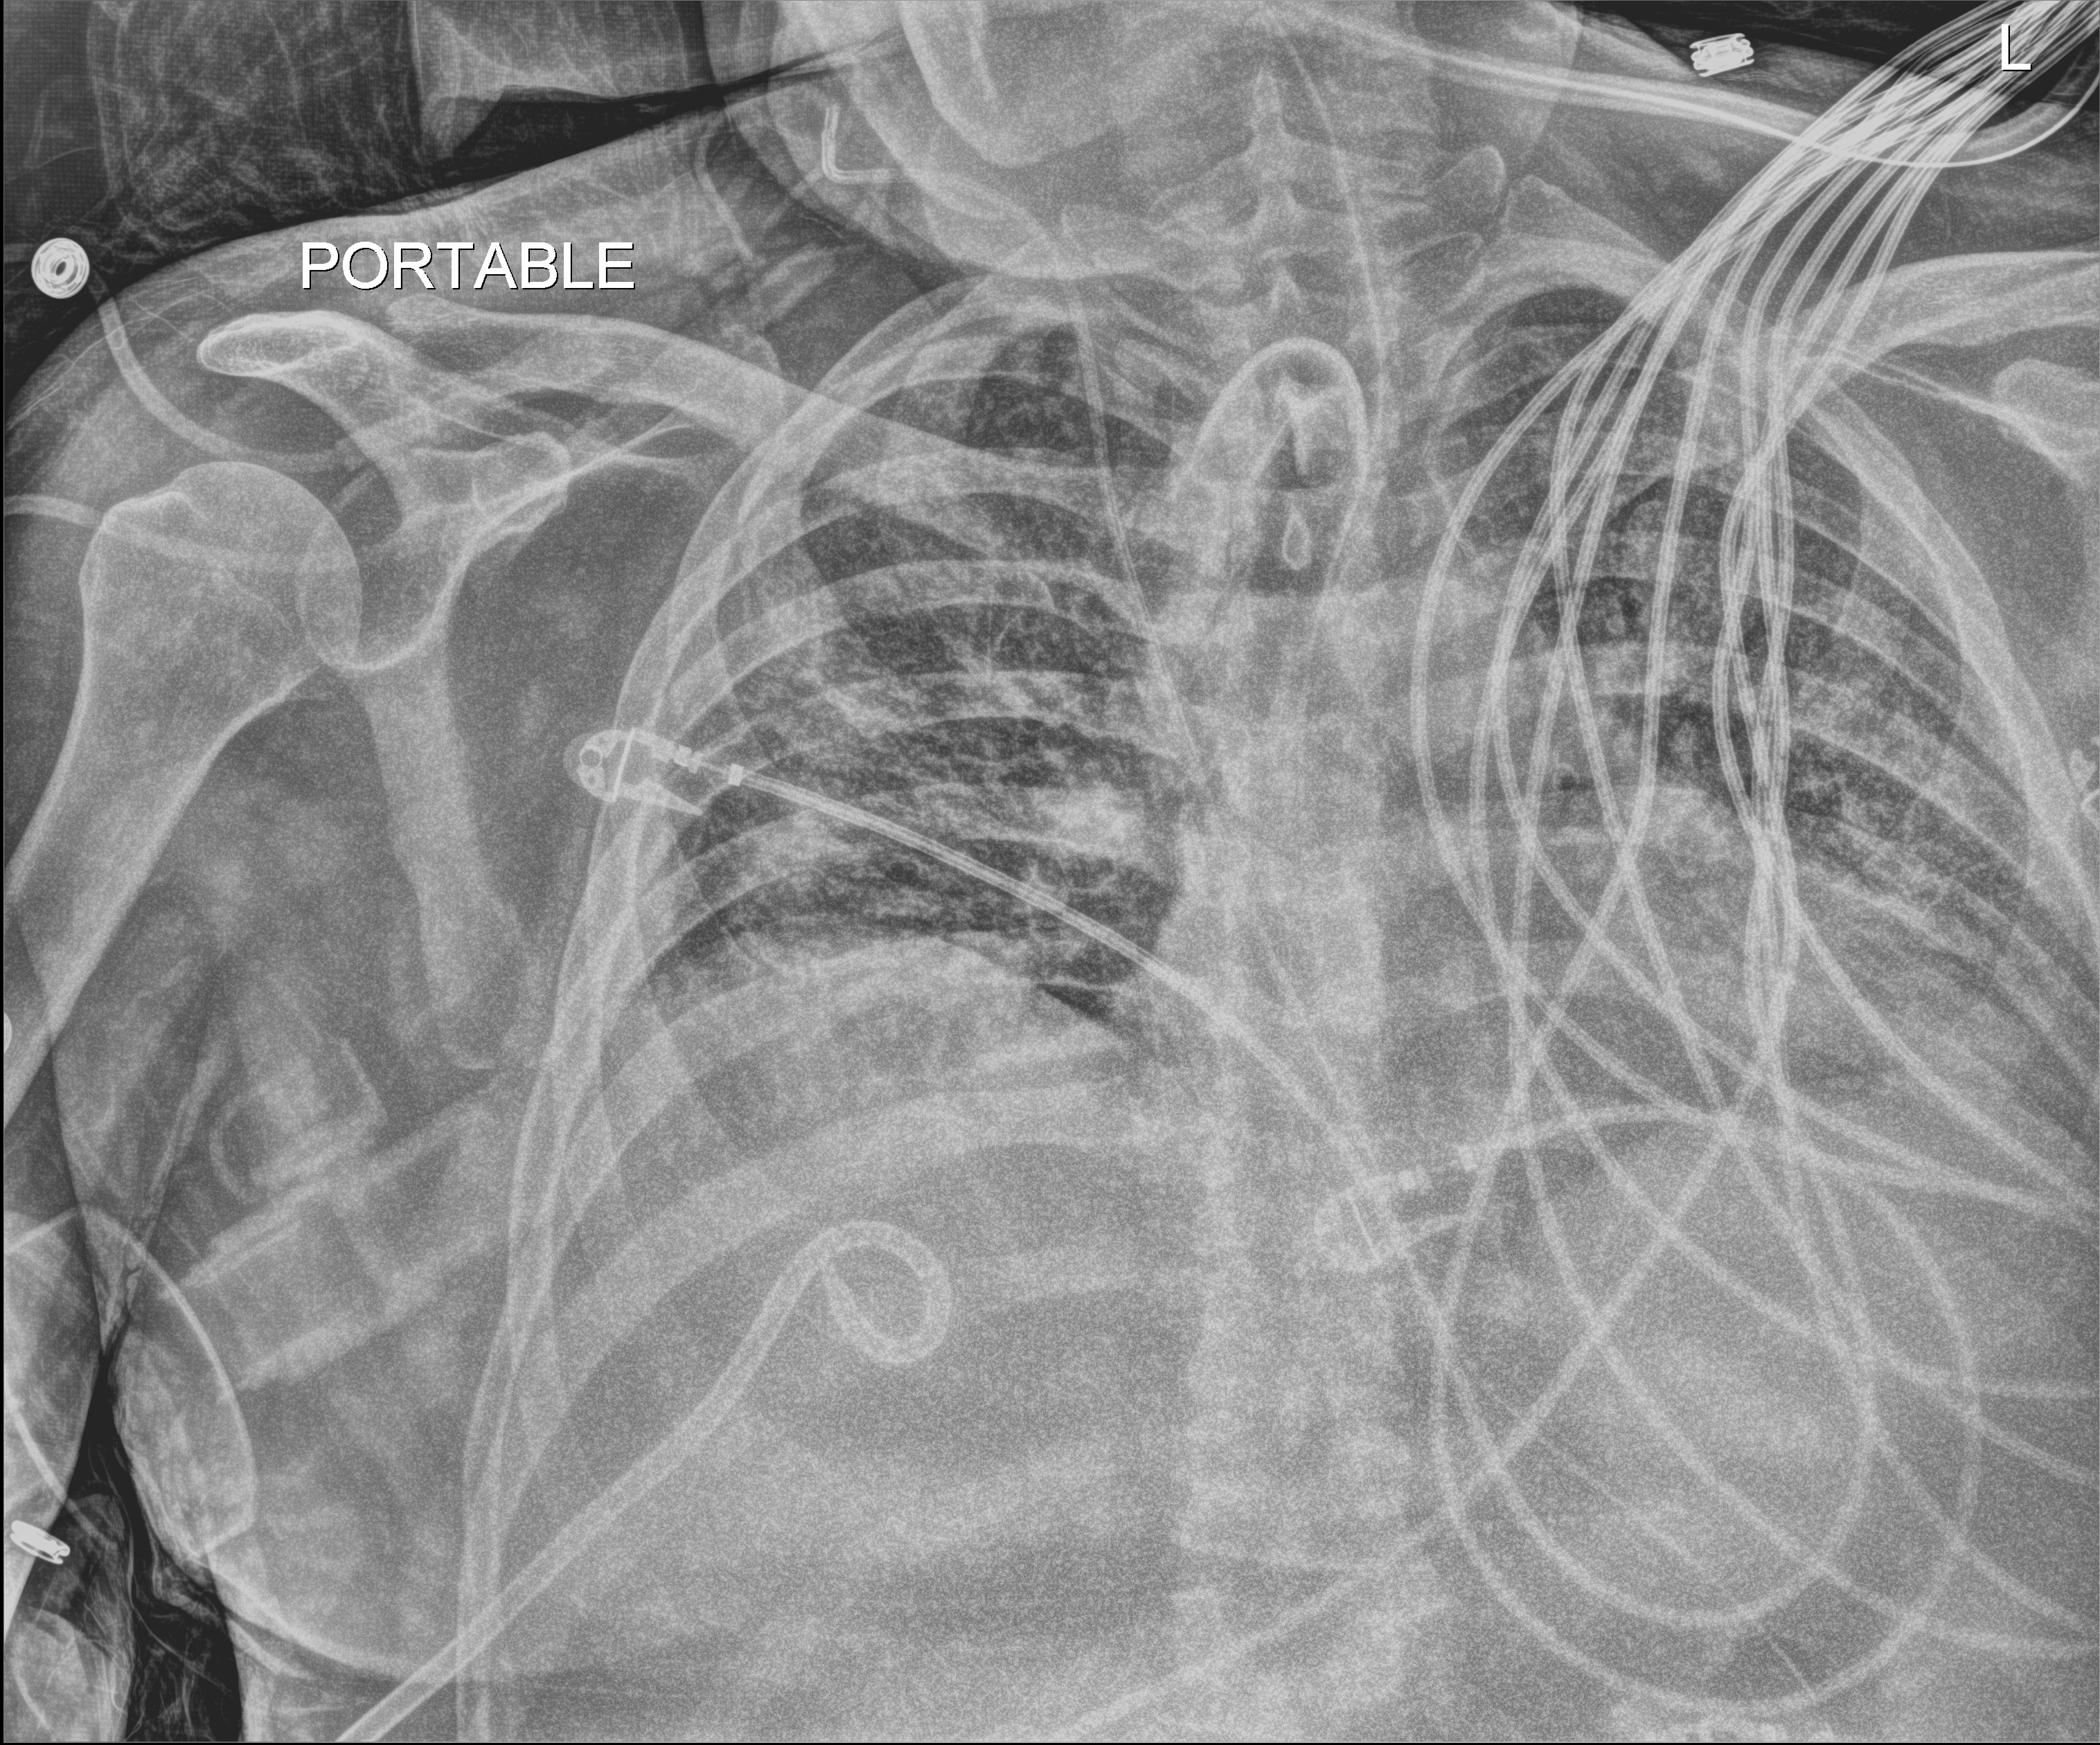
Bedside chest radiograph (digital radiography), anteroposterior (AP) projection. Patient hospitalised with COVID-19; male, aged 18–59 years.
Admission-level facts for this patient (not findings on this image; timing relative to this image not recorded): admitted to intensive care during this hospital stay: yes; mechanically ventilated during this hospital stay: yes.